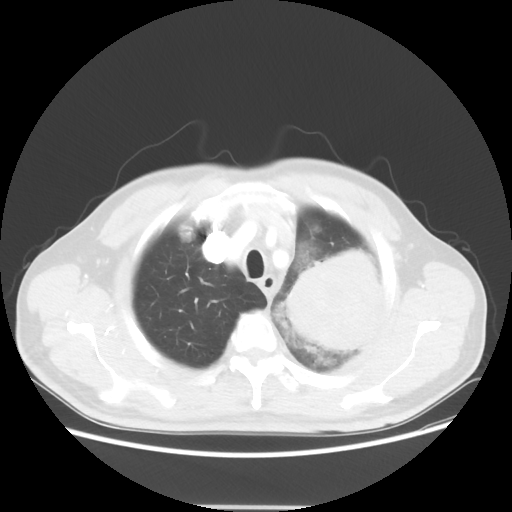
Chest CT, one axial slice; slice 46 of 53 in the series (ordered by position); reconstruction kernel STANDARD; lung window (W 1500 / L -600 HU); 5 mm slice thickness; 512 × 512 image matrix, field of view 391 × 391 mm. Patient: male, 60 years. From the clinical record (not read from this slice): clinical TNM (as recorded): T4 N1 M1a.
Annotated regions visible in this slice (bounding box drawn by a radiologist):
- lung tumour (recorded histology: large cell carcinoma): bounding box <281,241,389,363> (left, top, right, bottom; pixels)